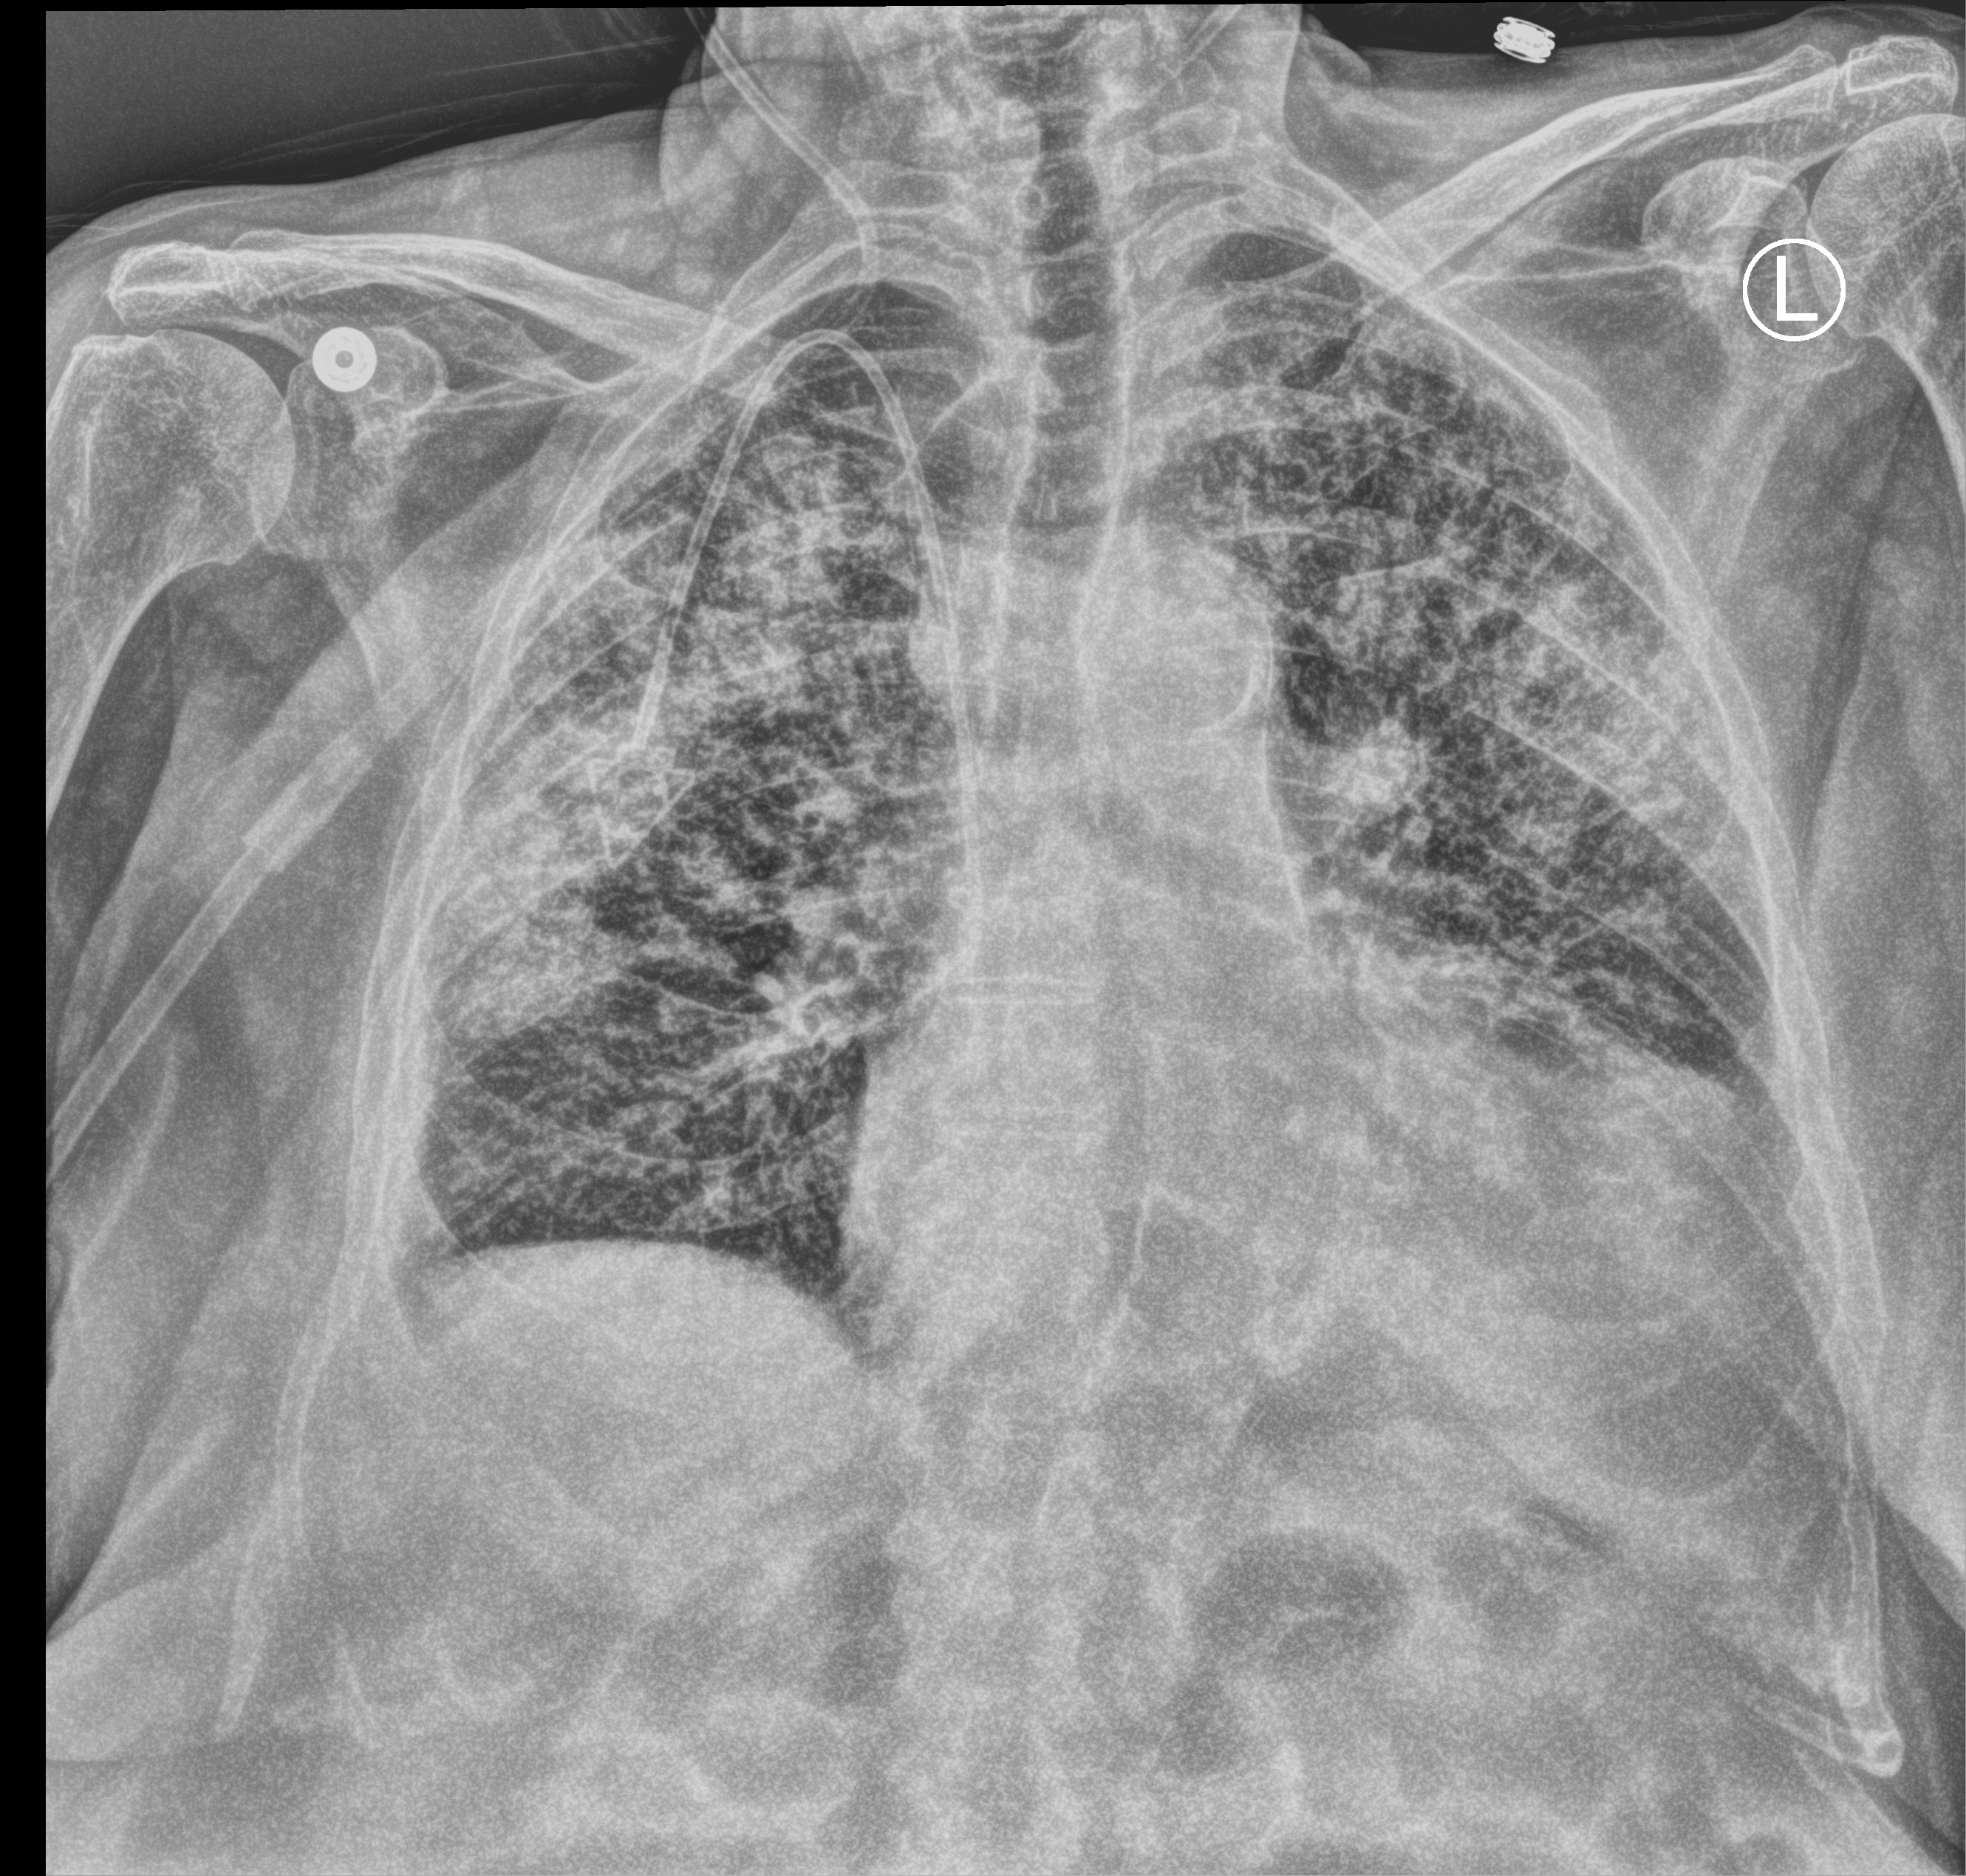
Bedside chest radiograph (computed radiography); anteroposterior (AP) projection. Female patient hospitalised with COVID-19, age 75–90 years.
From the hospital-stay record, not from the radiograph (when in the stay this image was taken is not recorded):
- mechanically ventilated during this hospital stay: no
- admitted to intensive care during this hospital stay: no